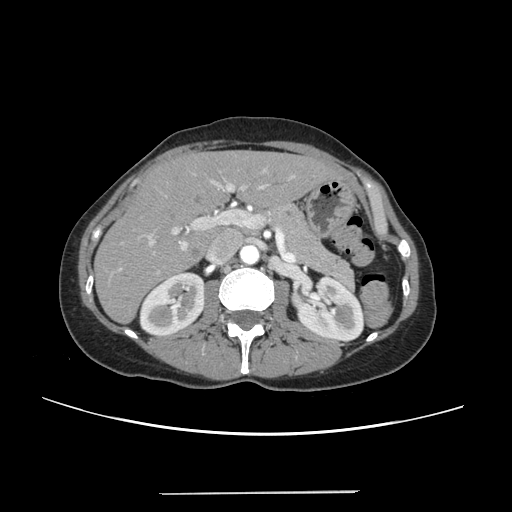
Contrast-enhanced abdominal CT, one axial slice. Slice 135 of 240 in the series (ordered by position). Soft-tissue window (W 400 / L 40 HU). 512 × 512 image matrix. Female patient, age 60 years. From the clinical record (not read from this slice): diagnosis: colorectal cancer liver metastases, imaged before liver resection; multiple liver metastases: no; largest metastasis: 1.5 cm; disease in both lobes: no.
Annotated regions visible in this slice (manually delineated by an expert):
- liver: bounding box (x1, y1, x2, y2) in pixels: (95, 152, 337, 322)
- planned liver remnant (the part of the liver to remain after resection): (96, 152, 337, 322)
- portal vein (with intrahepatic branches): (118, 169, 293, 274)